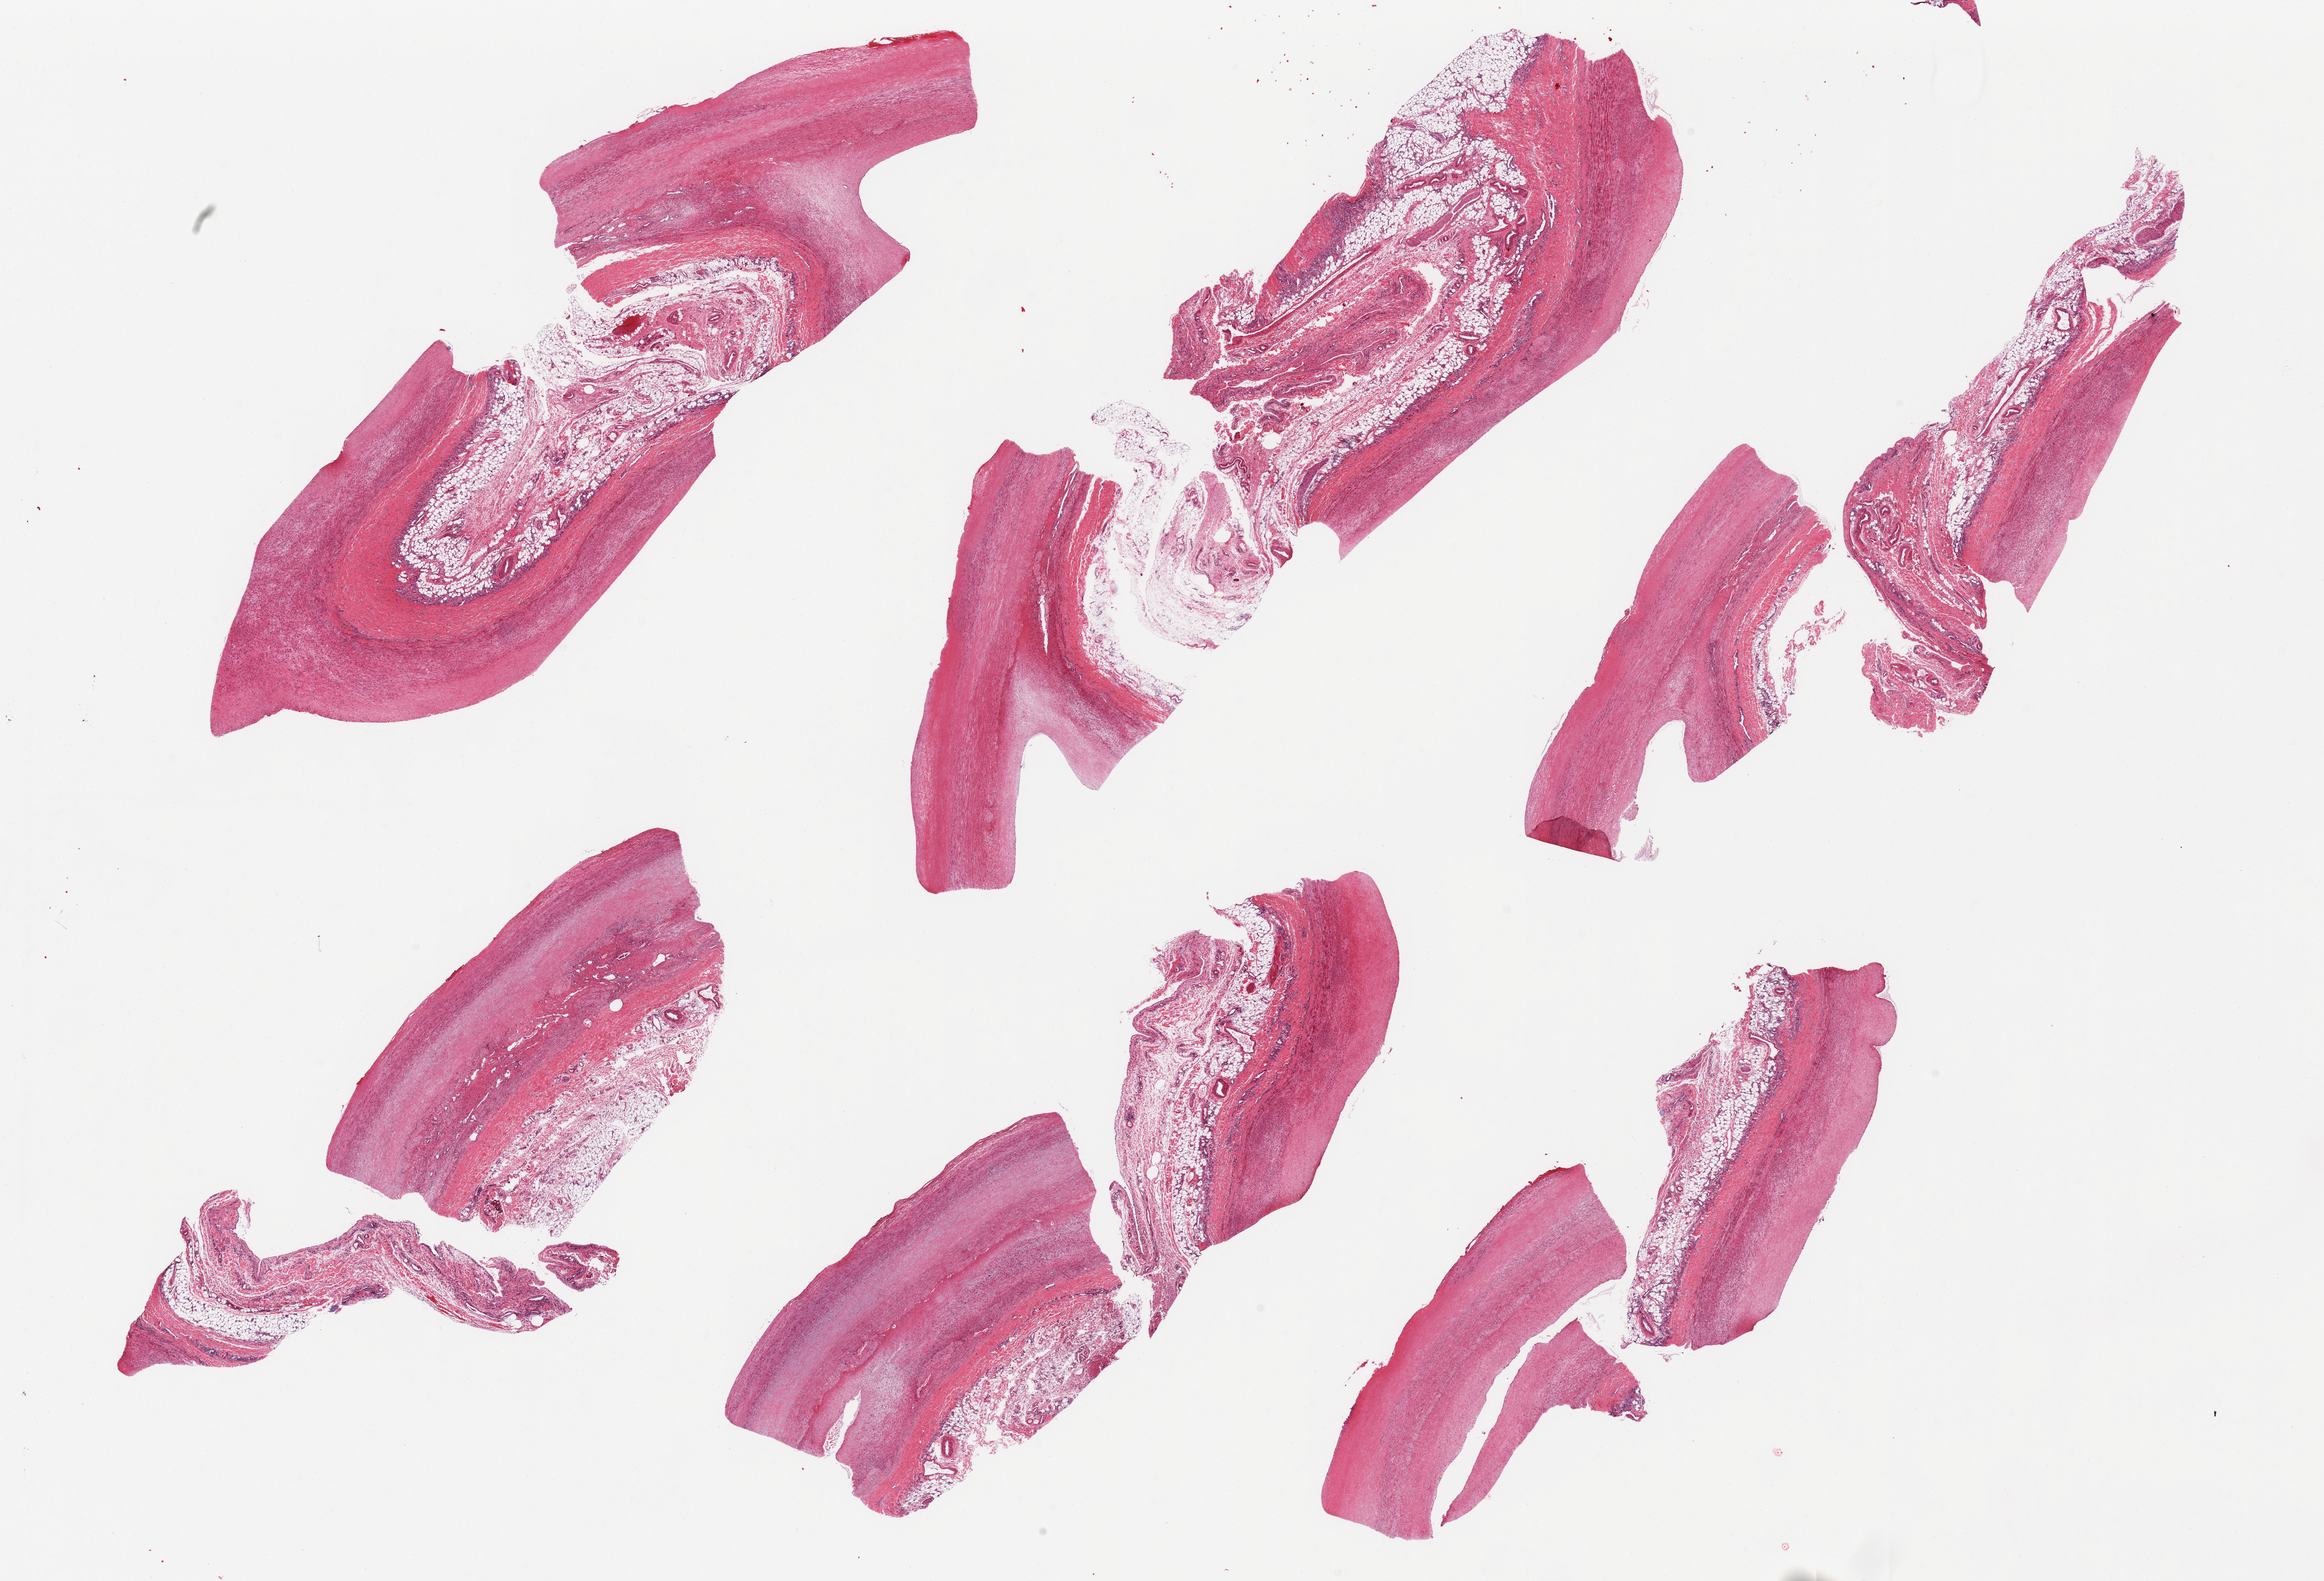
Whole-slide image, H&E stain, brightfield — low-resolution overview of the scanned area, about 31.5 x 21.4 mm (from a 20x scan). PAXgene-fixed, paraffin-embedded tissue. Target tissue: aorta. Tissue donor sample. Donor: male.
Review note (as recorded): 10 pieces; up to 1.5 mm adventitial fat.